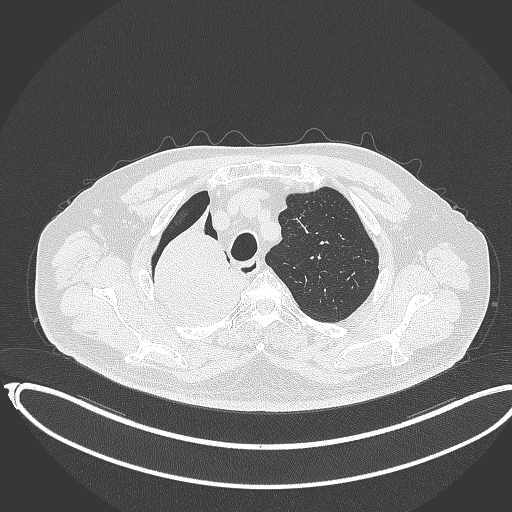
Chest CT, one axial slice. Slice 301 of 403 in the series (ordered by position). Reconstruction kernel B70f. 120 kVp. Lung window (W 1500 / L -600 HU). 512 × 512 image matrix. Male patient, age 68 years. From the clinical record (not read from this slice): clinical TNM (as recorded): T2a N0 M0.
Annotated regions visible in this slice (bounding box drawn by a radiologist):
- lung tumour (recorded histology: adenocarcinoma): bounding box (x1, y1, x2, y2) in pixels: (144, 209, 250, 333)